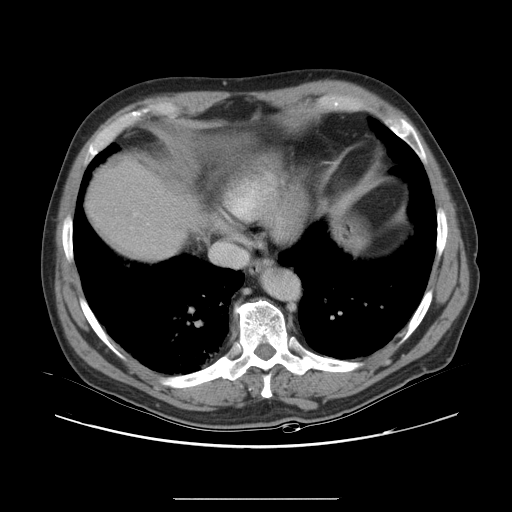
Contrast-enhanced abdominal CT, one axial slice; position 30 of 40 along the scan axis; 120 kVp; intravenous contrast given; soft-tissue window (W 400 / L 40 HU); 5 mm slice thickness; 512 × 512 image matrix, field of view 408 × 408 mm. Male patient, age 64 years. Case-level facts recorded for this patient, not image findings: diagnosis: colorectal cancer liver metastases, imaged before liver resection.
Structures marked on this image (manually delineated by an expert):
- liver: bounding box <88,162,192,262> (left, top, right, bottom; pixels)
- planned liver remnant (the part of the liver to remain after resection): <88,162,193,260>